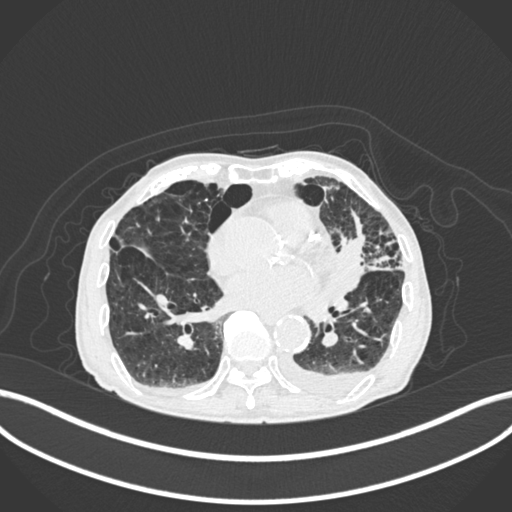
Chest CT, one axial slice; slice 84 of 400 in the series (ordered by position); reconstruction kernel B30f; 120 kVp; lung window (W 1500 / L -600 HU); 512 × 512 image matrix, field of view 400 × 400 mm. Male patient, age 90 years or older. Case-level facts recorded for this patient, not image findings: clinical TNM (as recorded): T2b N1 M0.
Outlined on this slice (rectangle marked by the reading radiologist):
- lung tumour (recorded histology: squamous cell carcinoma): bounding box [x1, y1, x2, y2] px = [337, 225, 365, 290]